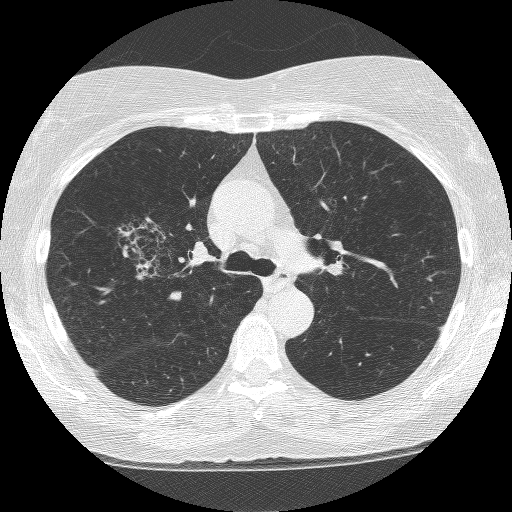
Chest CT (low-dose screening protocol), one axial image, second annual screen, lung window (W 1500 / L -600 HU), 120 kVp, 512 × 512 image matrix. Female, age 64 years at enrolment. Former smoker at enrolment.
Expert-annotated lung lesion, box from (x=115, y=204) to (x=210, y=293) px. The screening reader recorded 4 non-calcified nodules or masses ≥4 mm on this exam; which of them this box marks is not recorded.